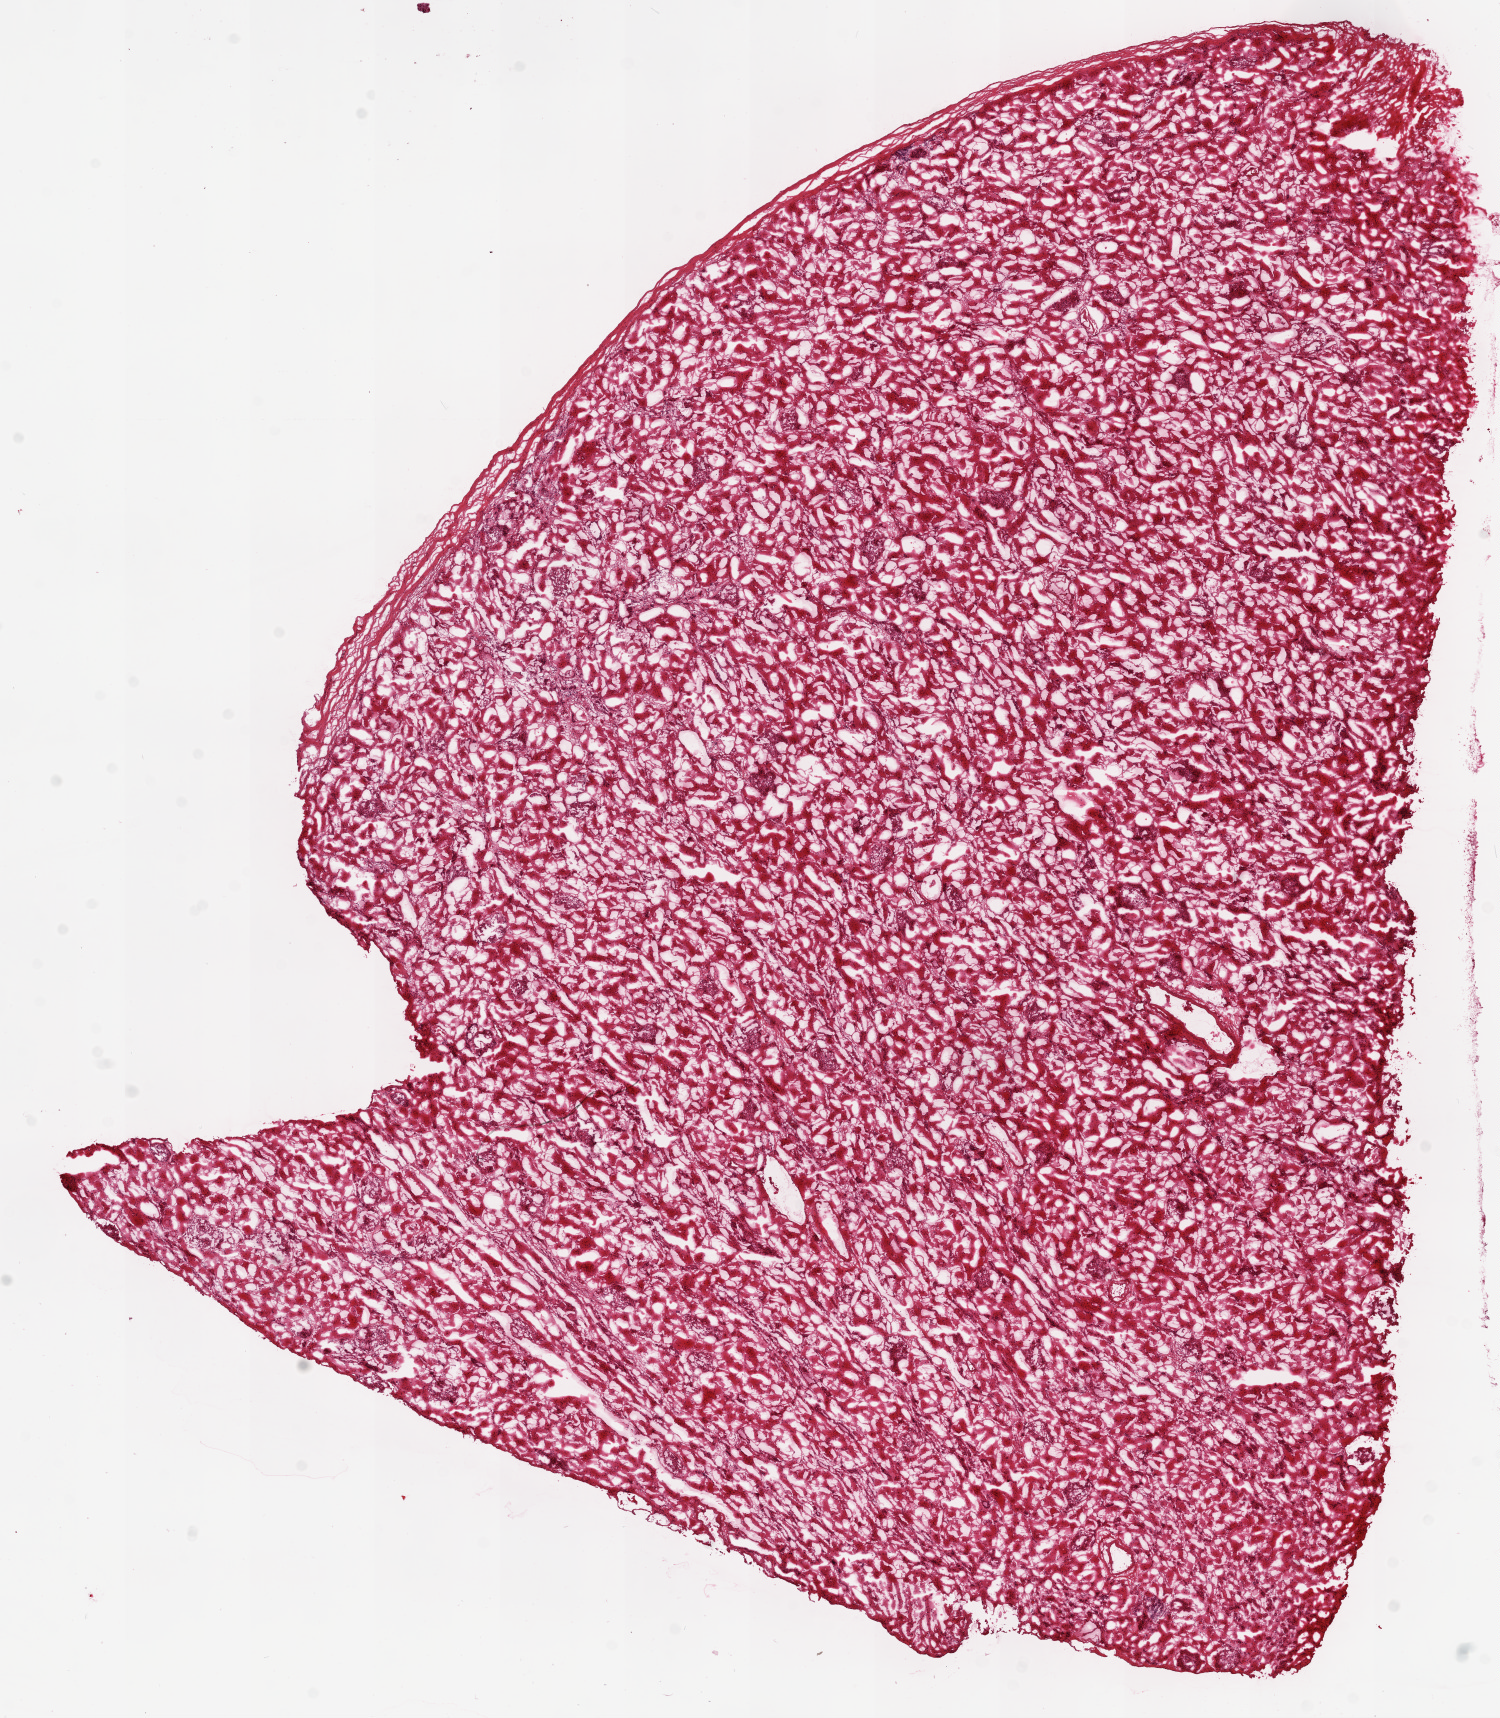
Whole-slide histology image, H&E — shown as a low-resolution overview of the whole scanned area (about 12.0 x 13.8 mm); frozen section from the top of the tissue portion; solid tissue normal (non-tumour tissue) sample from the kidney. Male patient; age at initial diagnosis 58 years.
This section: solid tissue normal (non-tumour) sample from the same patient. Patient diagnosis: Clear cell adenocarcinoma, NOS.